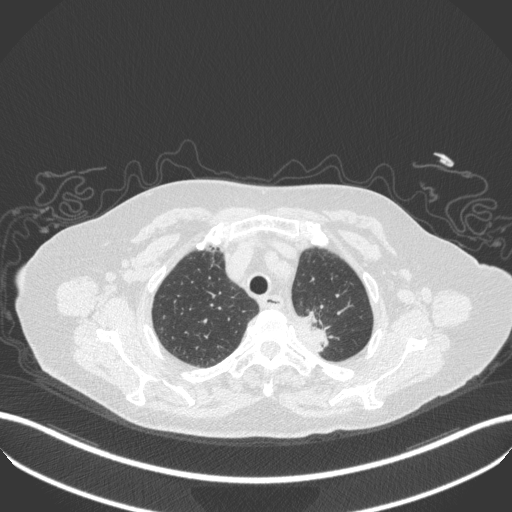
Chest CT, one axial slice; position 283 of 353 along the scan axis; 100 kVp; lung window (W 1500 / L -600 HU); 512 × 512 image matrix, field of view 400 × 400 mm. Patient: female, 81 years. From the clinical record (not read from this slice): clinical TNM (as recorded): T2a N0 M0.
Outlined on this slice (rectangle marked by the reading radiologist):
- lung tumour (recorded histology: adenocarcinoma): bounding box [x1, y1, x2, y2] px = [280, 307, 342, 368]